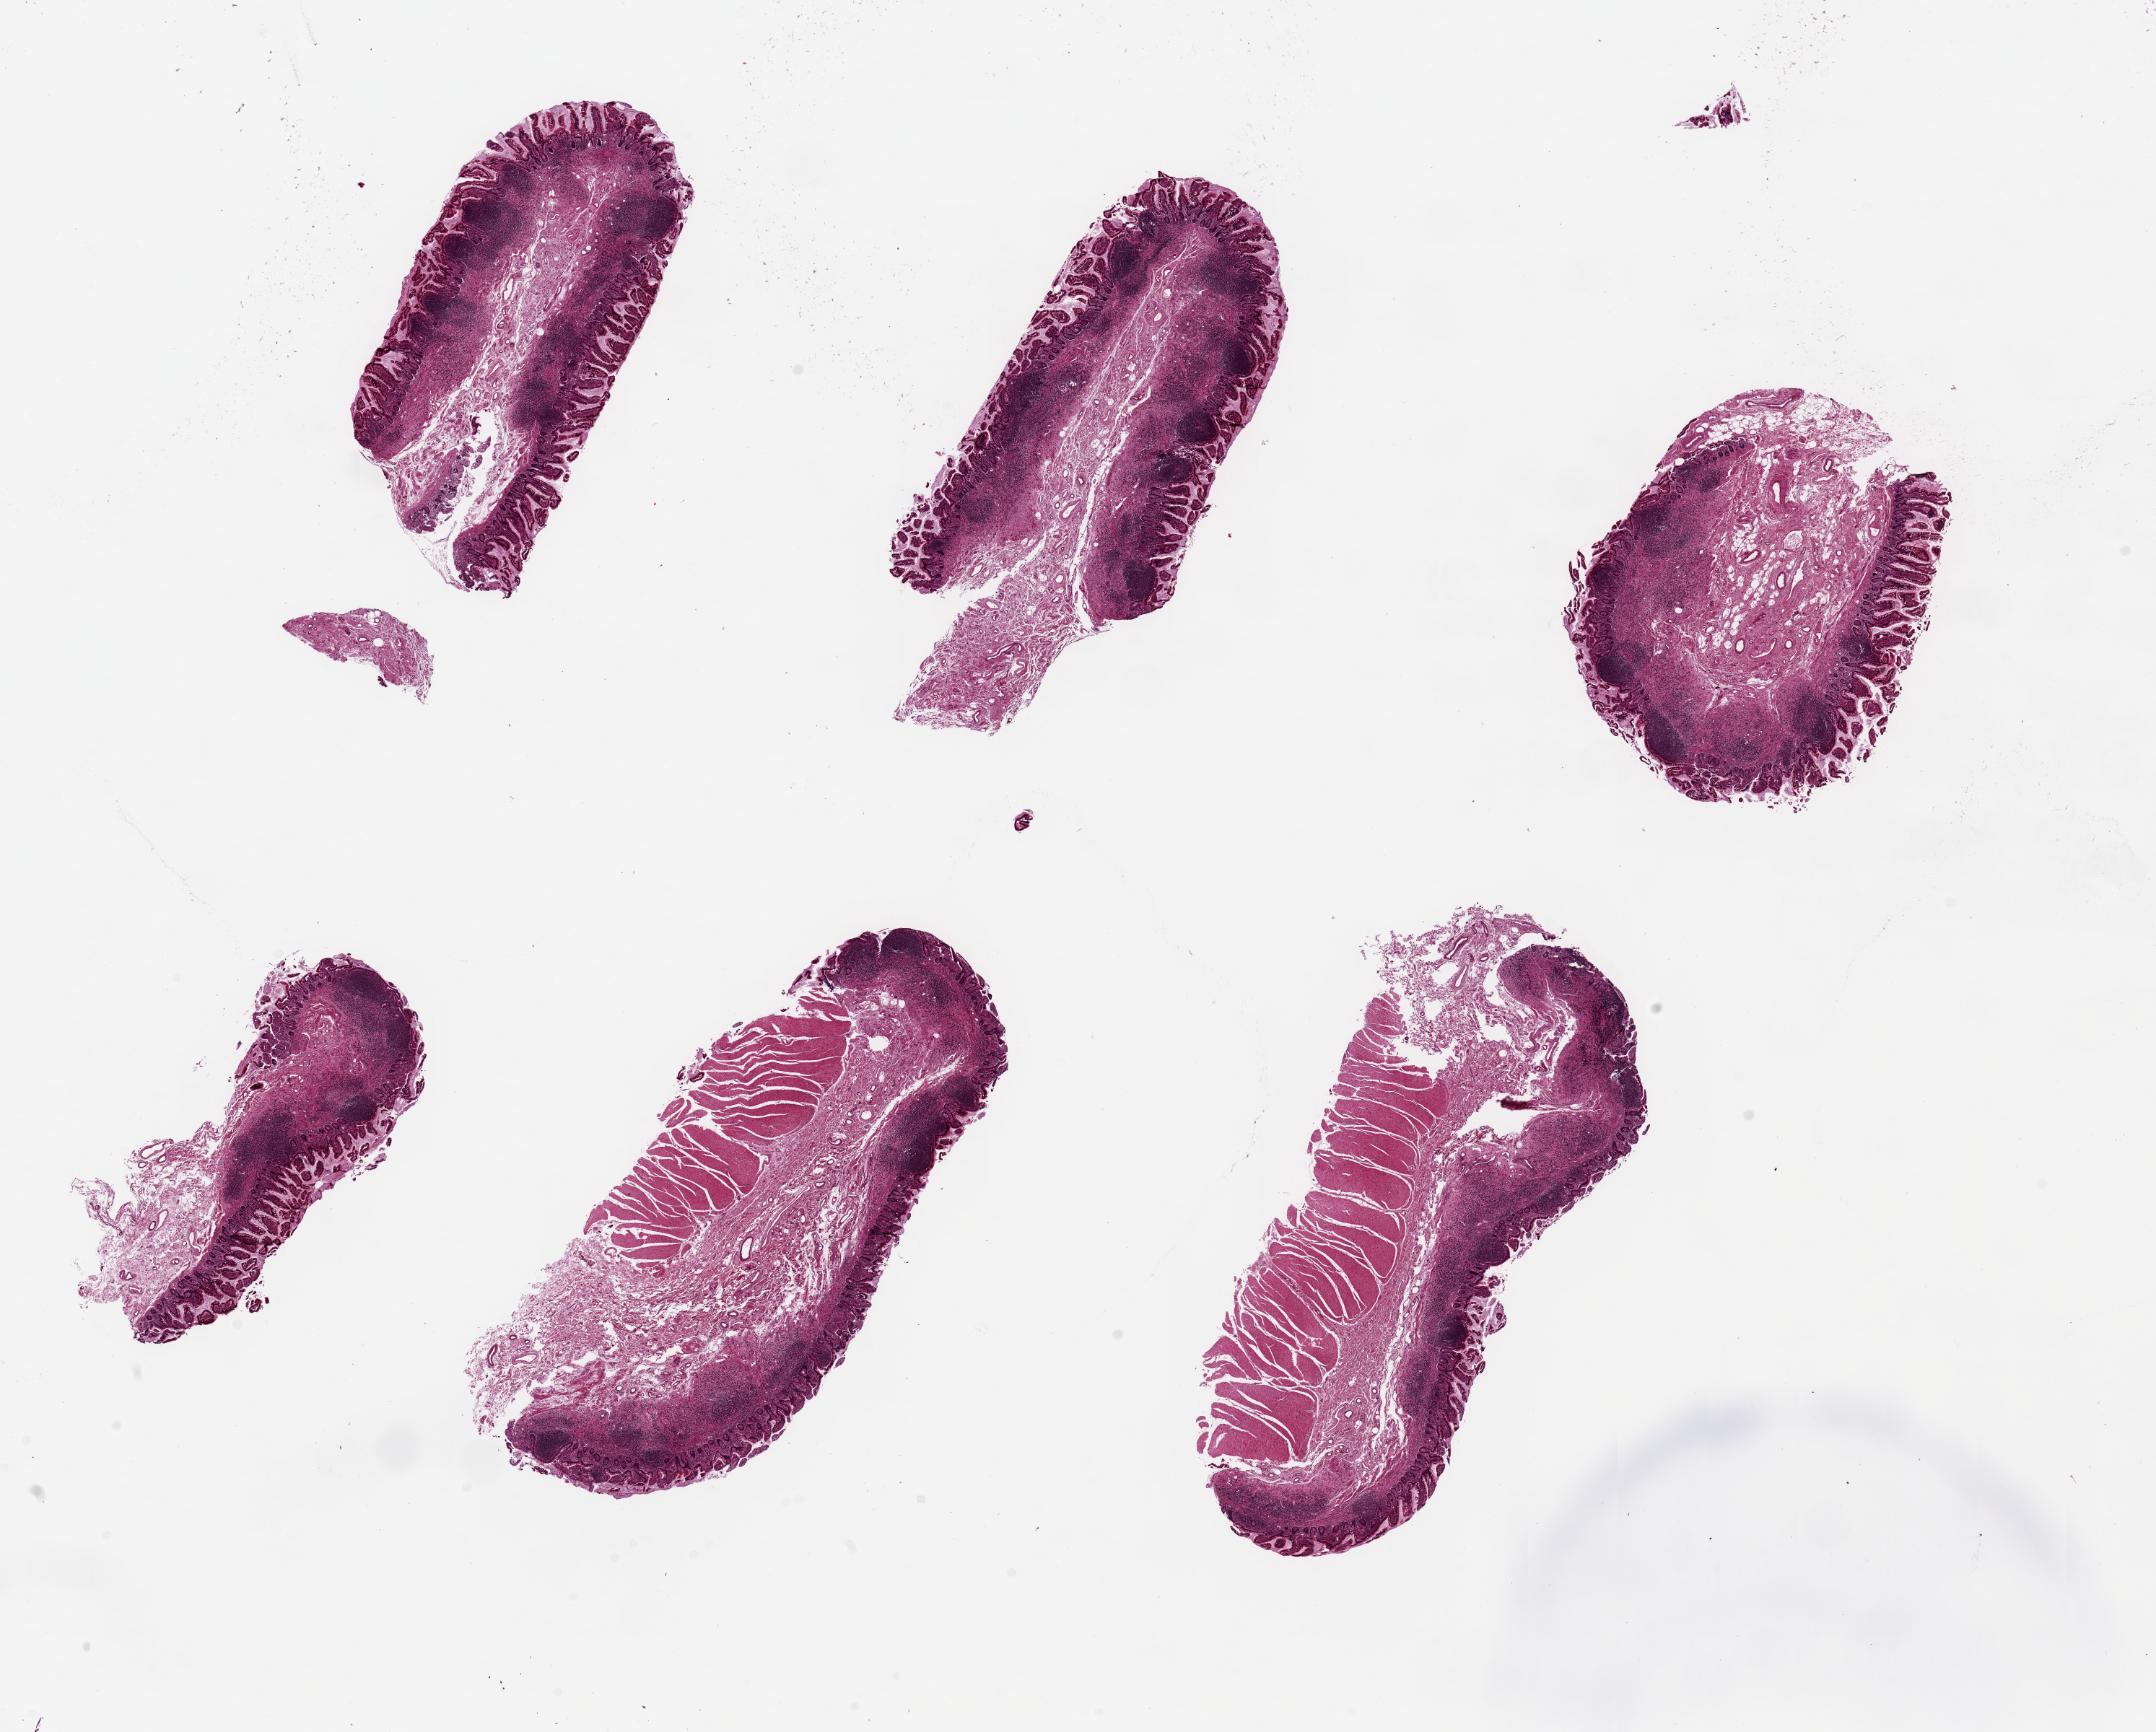
Digitized haematoxylin and eosin-stained section — a low-resolution overview of the entire scanned area, about 23.6 x 19.0 mm (slide scanned at 20x); PAXgene-fixed, paraffin-embedded tissue; section of ileum (target tissue); donor tissue sample. Male donor.
• review note (as recorded): 6 pieces, up to 7x4mm; ~5-10% lympohid elements, rest is mucosa and muscularis, well preserved